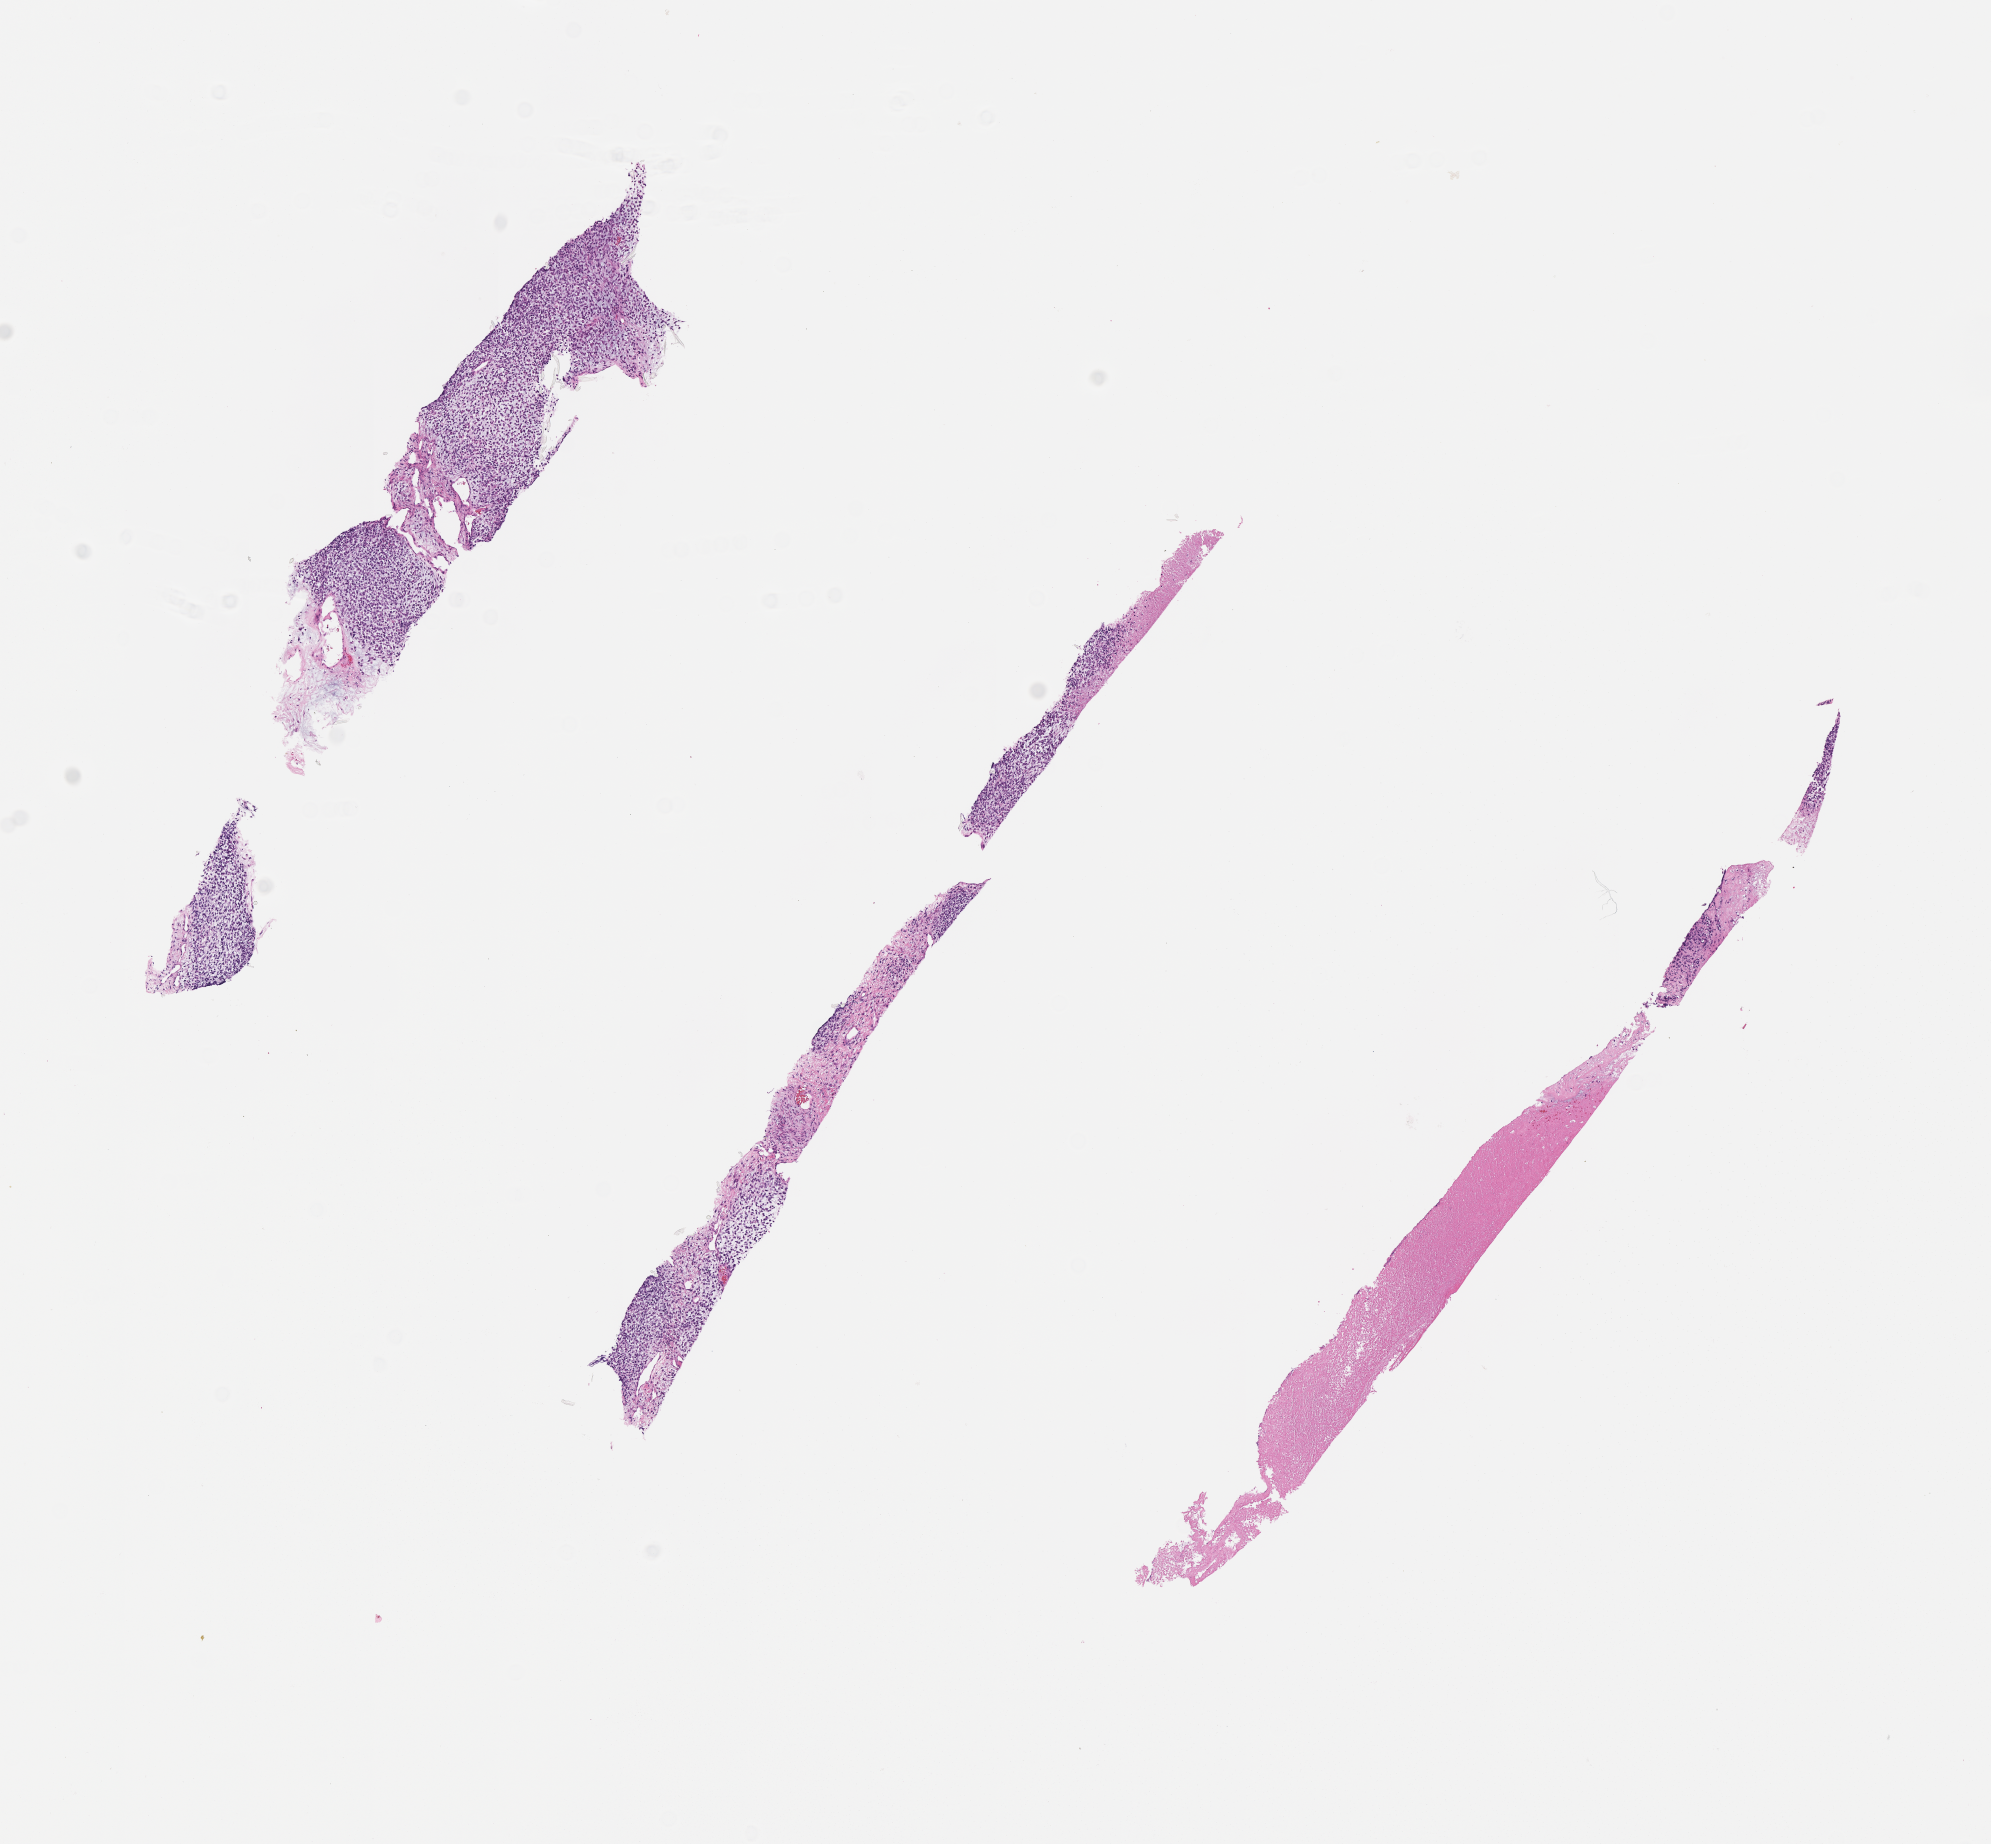
Digitized H&E-stained section of tumor tissue — low-resolution overview of the scanned area, about 8.1 x 7.5 mm. FFPE section. Site: prostate. Male patient, age at diagnosis 13.1 years.
Diagnosis: rhabdomyosarcoma; histological classification: embryonal rhabdomyosarcoma. Stage (as recorded): 3.